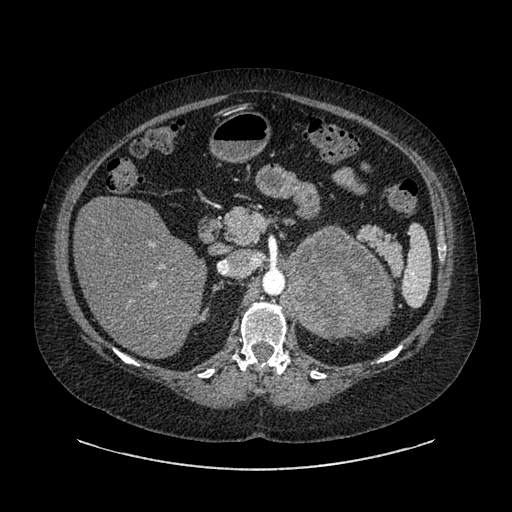
Contrast-enhanced abdominal CT, one axial slice. Reconstruction kernel SOFT. 120 kVp. Soft-tissue window (W 400 / L 40 HU). 0.62 mm slice thickness. 512 × 512 image matrix, field of view 460 × 460 mm. Female patient, age 61 years. From the clinical record (not read from this slice): diagnosis: adrenocortical carcinoma; tumour side: left adrenal; tumour size at pathology: 13 cm; Ki-67 index: 79 %; stage (as recorded): 2.
Outlined on this slice (semi-automatically segmented with operator editing):
- mass: bounding box (x1, y1, x2, y2) in pixels: (281, 229, 390, 339)